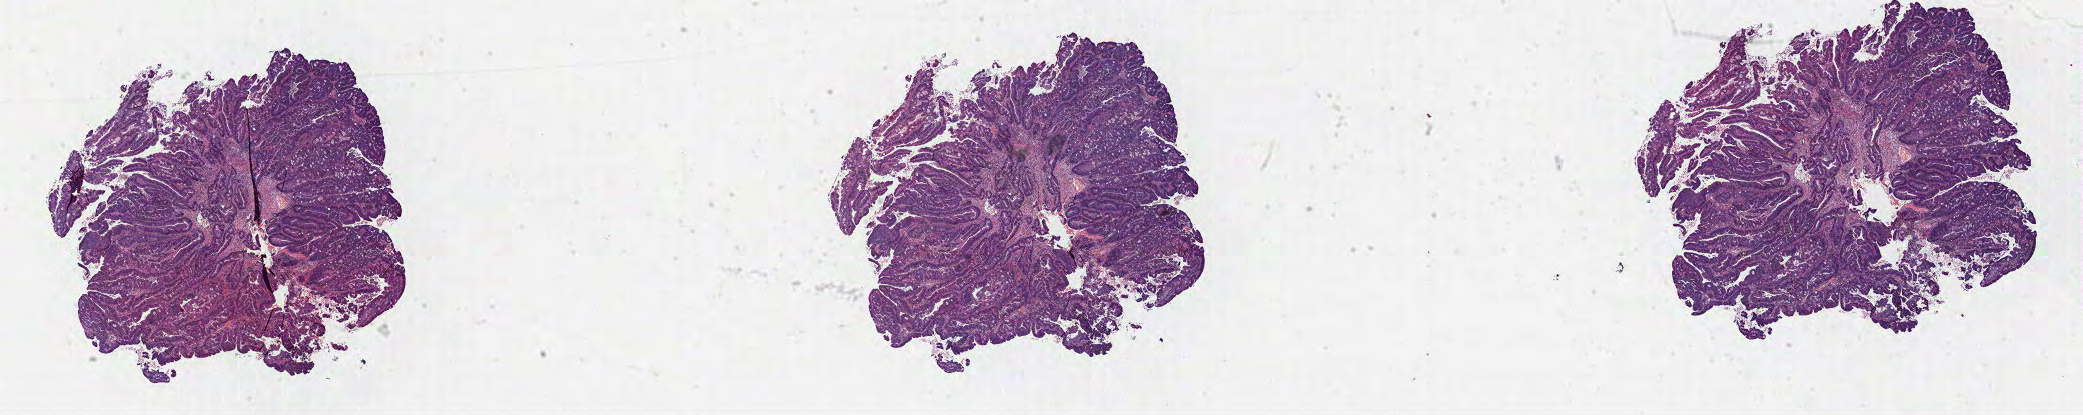
H&E-stained whole-slide image — whole scanned area (about 33.6 x 6.7 mm, acquisition: 40x scan) shown as a low-resolution overview, formalin-fixed paraffin-embedded (FFPE) diagnostic section, sample: primary tumour, colon. Patient: female, age at initial diagnosis 57 years.
* lymph nodes positive (case pathology): 0 of 25 examined
* diagnosis: Adenocarcinoma, NOS (ascending colon)
* AJCC pathologic stage: IV